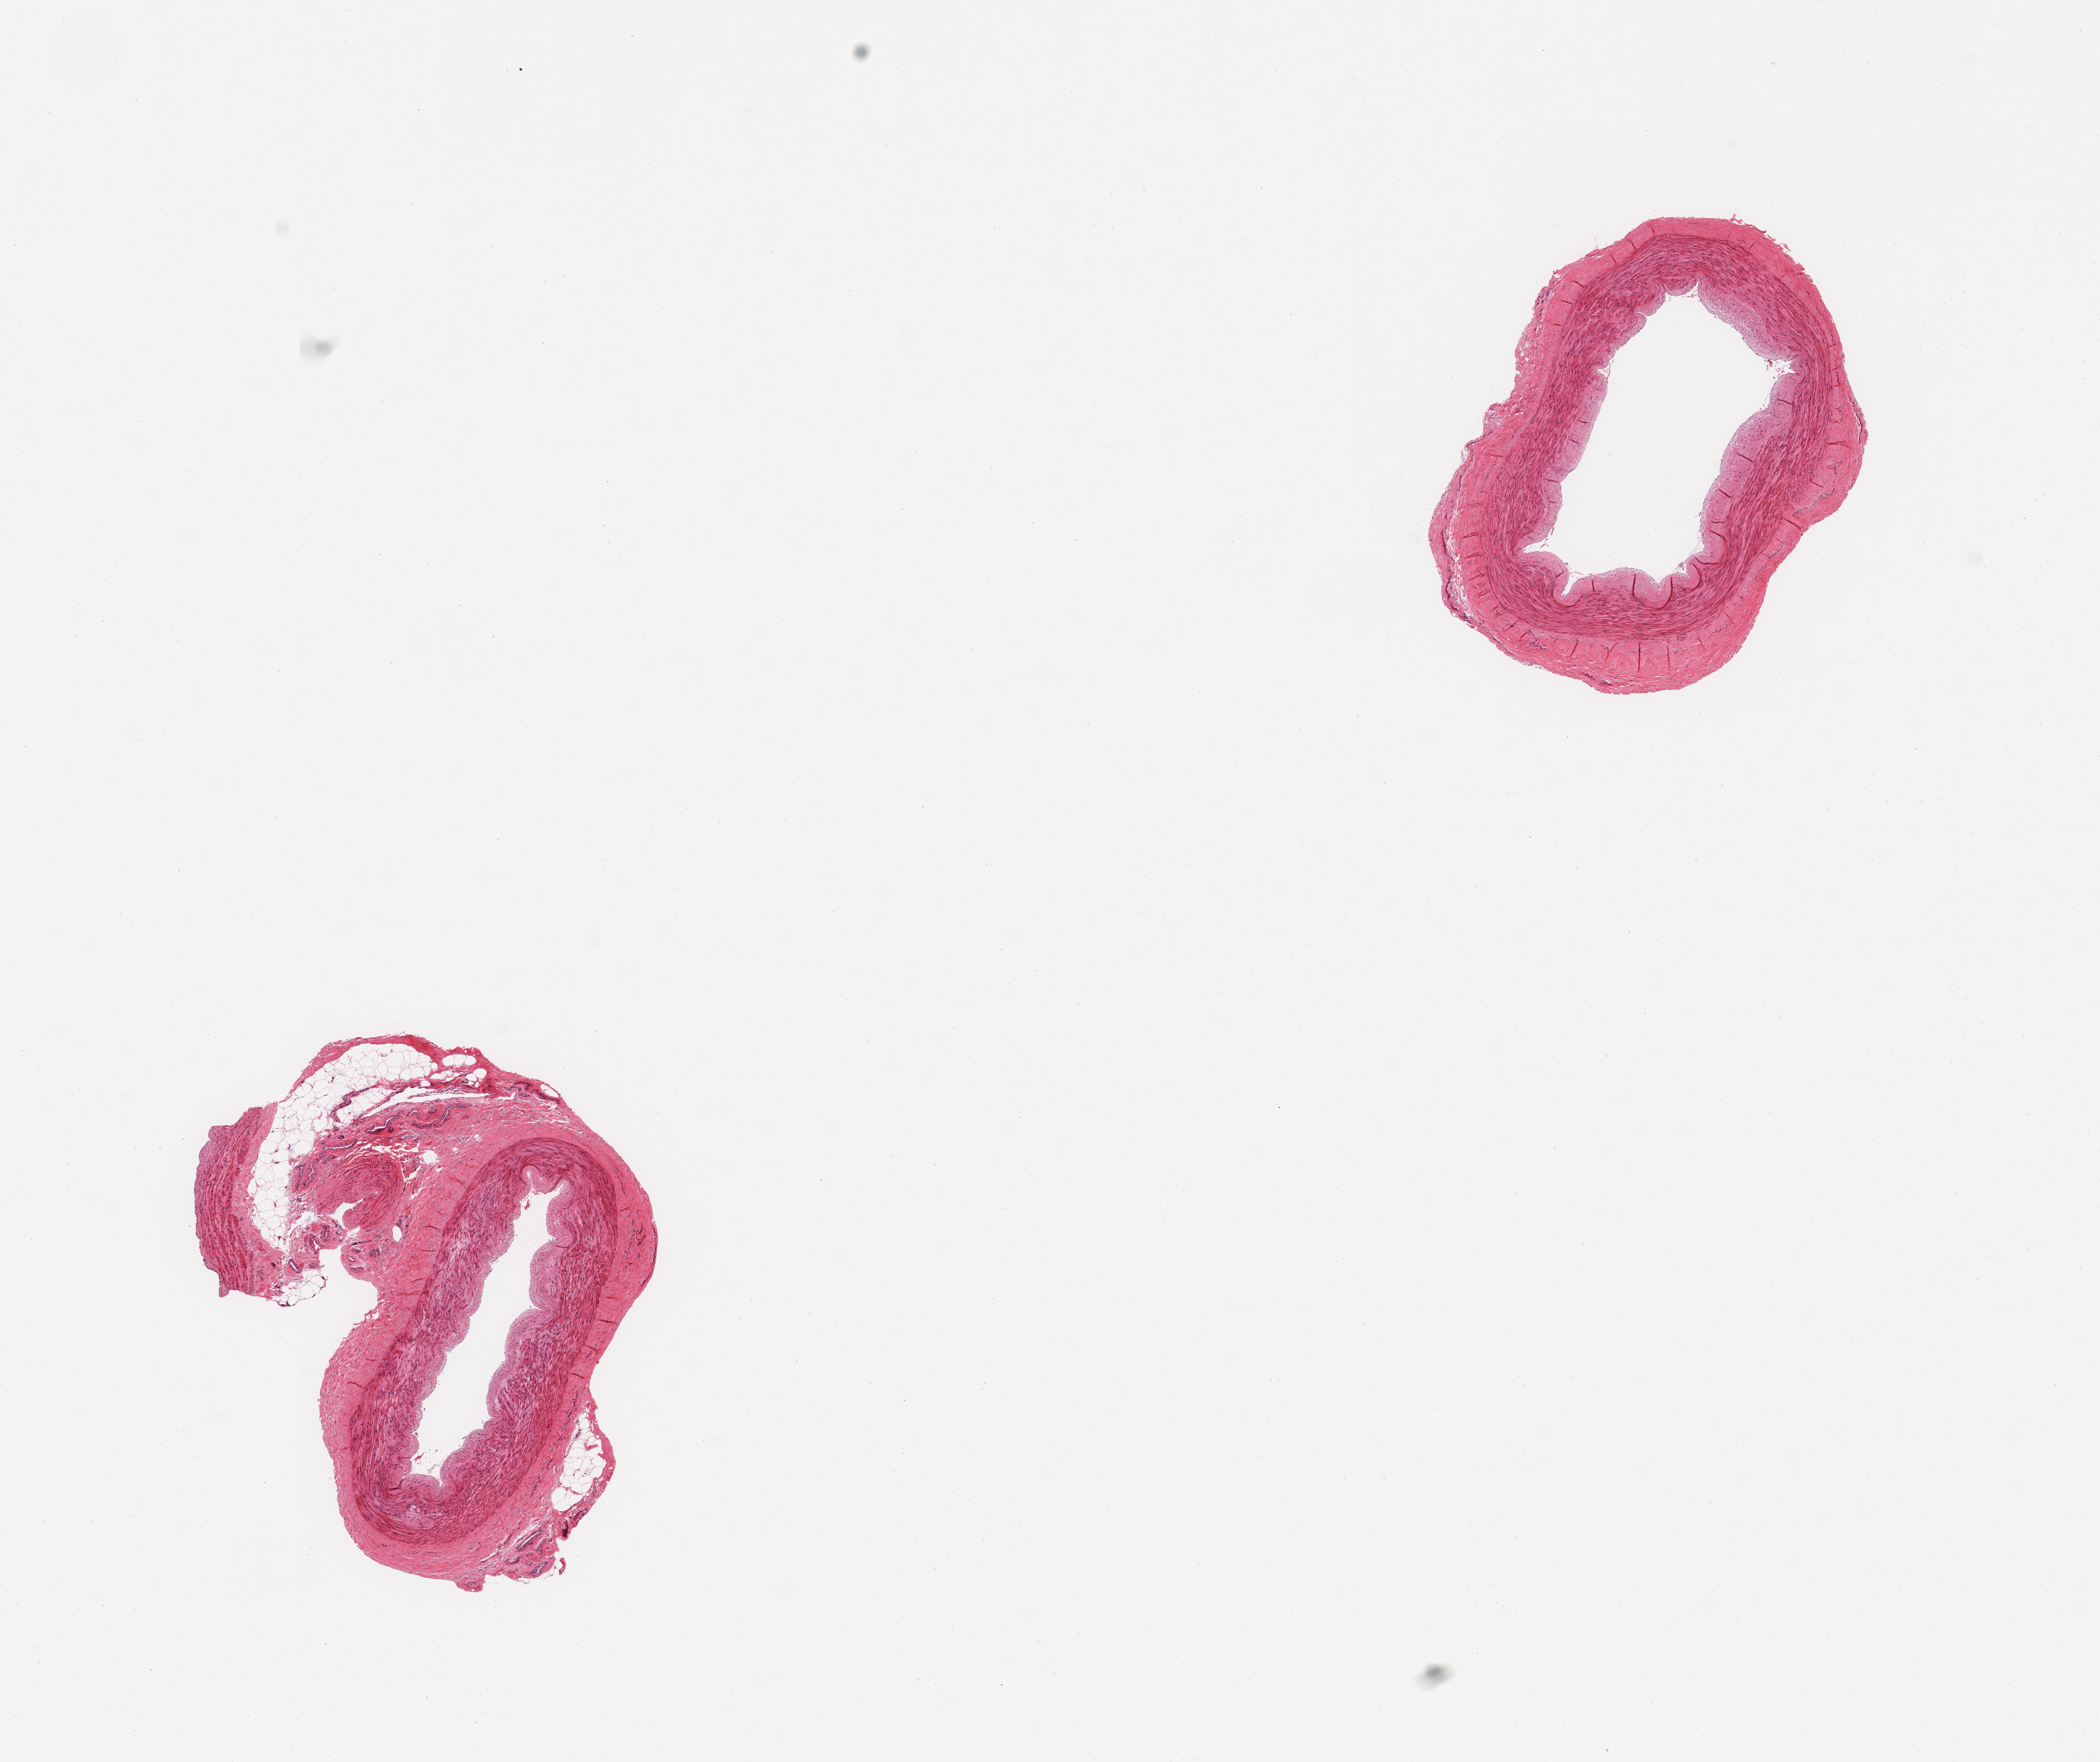
Whole-slide image, hematoxylin and eosin (H&E) stain — whole scanned area (about 13.8 x 11.6 mm, slide scanned at 20x) shown as a low-resolution overview. Donor sex: male.
- specimen: PAXgene-fixed, paraffin-embedded tissue; target tissue: tibial artery; donor tissue sample